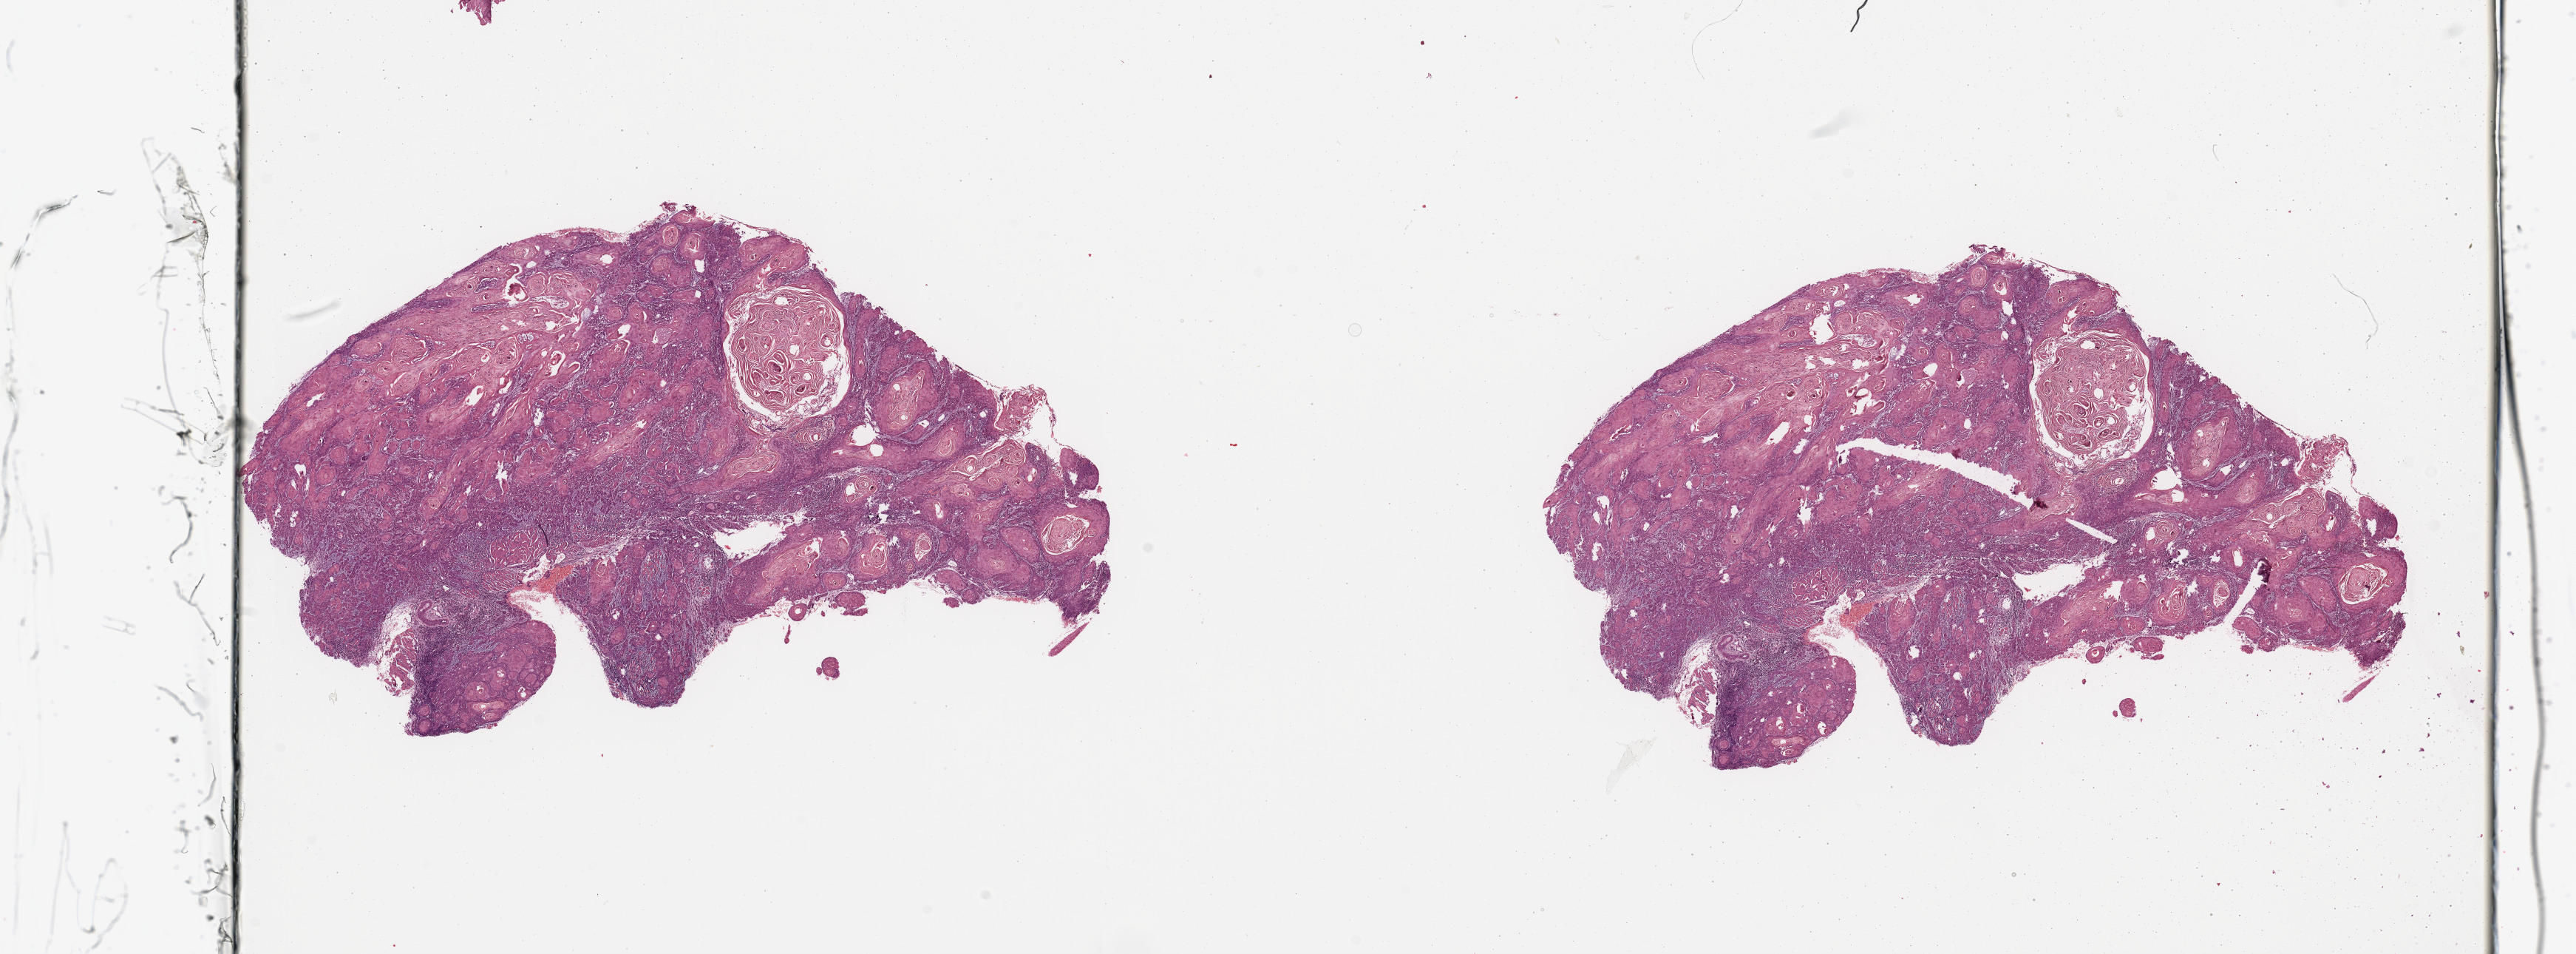
Whole-slide histology image, Hematoxylin and eosin (H&E) stained, shown as a low-resolution overview of the whole scanned area (about 27.6 x 10.2 mm, acquisition: 20x scan). Tumour tissue sample, sampled site: tongue. Female, 60 y/o. Histologic grade: G1 (well differentiated). Composition of this section per pathologist review: tumour nuclei 80%, necrosis 5%.
Histologic diagnosis: Squamous cell carcinoma, NOS (tongue, NOS). Primary tumour site (as recorded): oral cavity. AJCC pathologic stage: III.